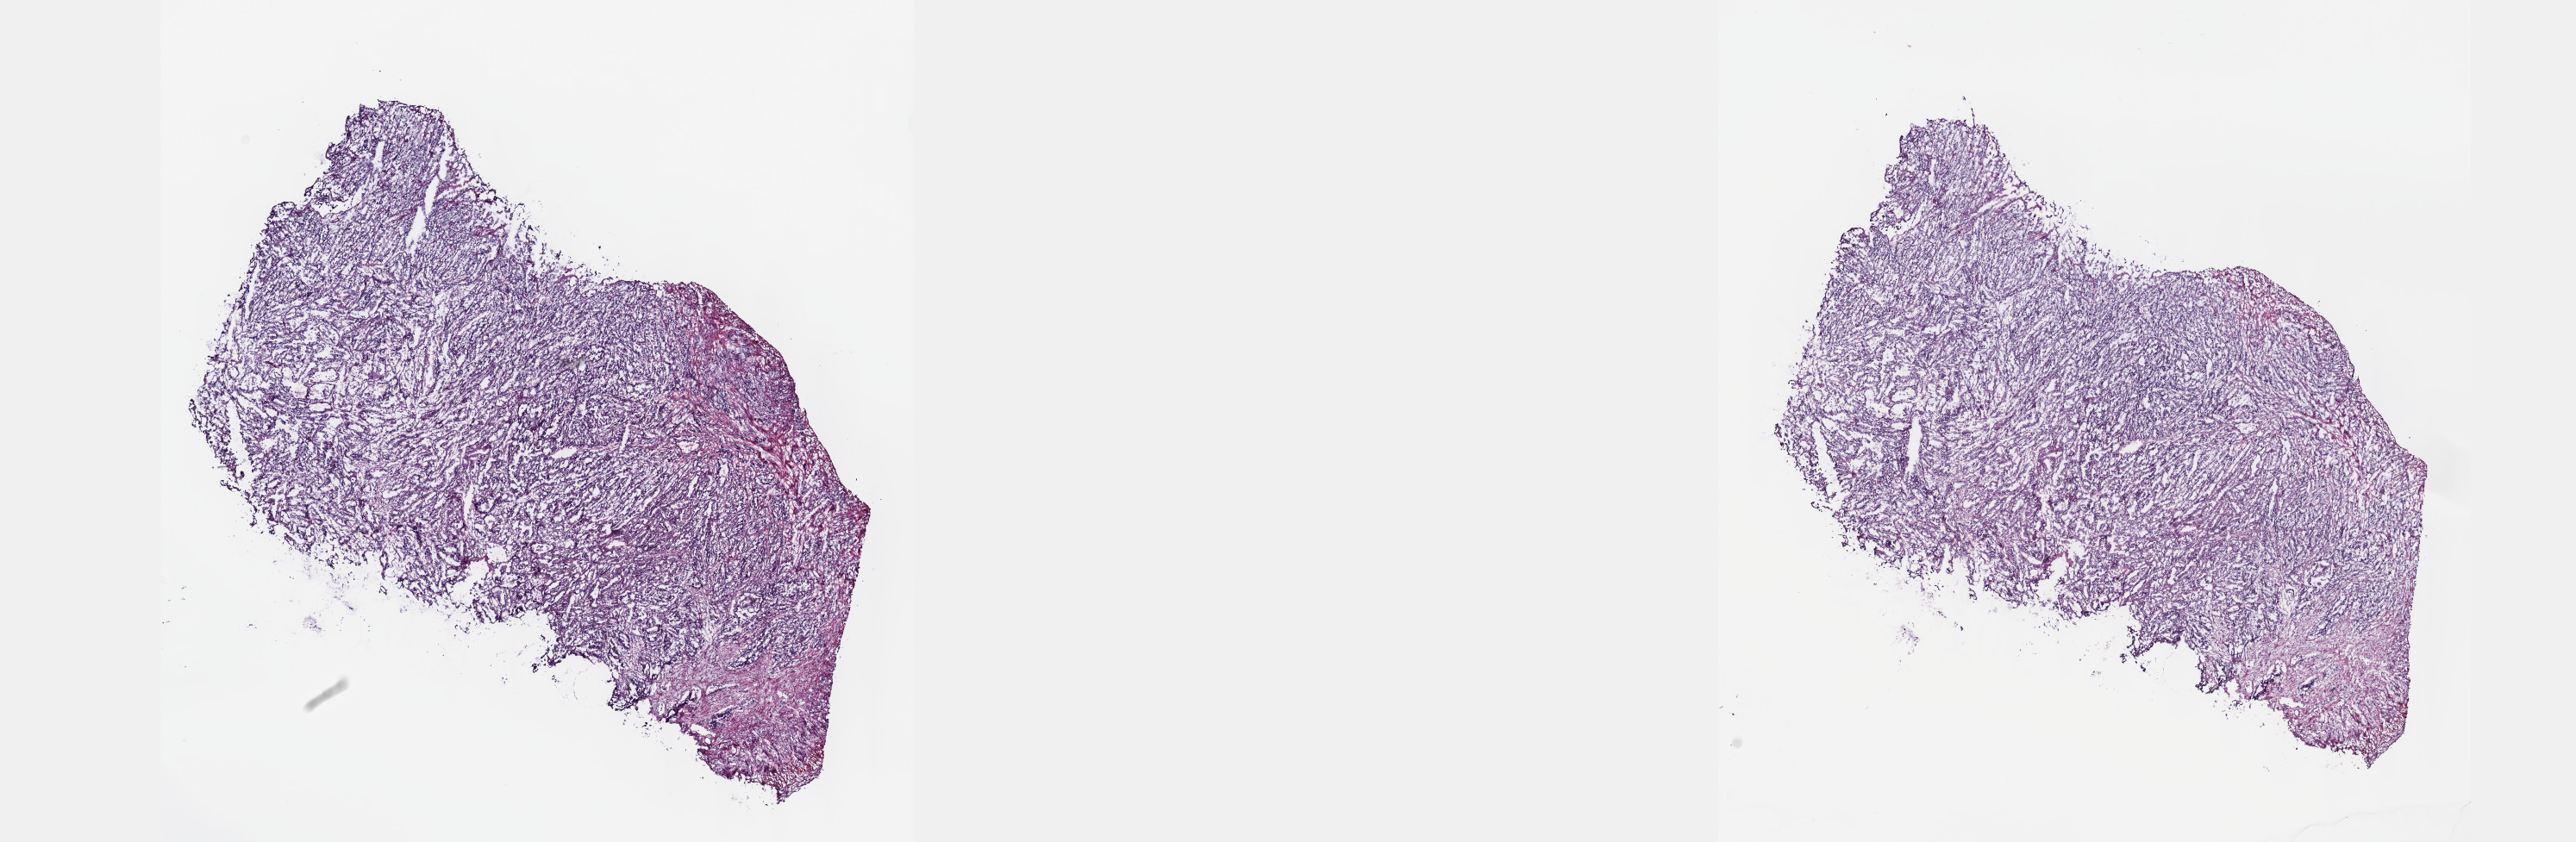
Whole-slide histology image, H&E — shown as a low-resolution overview of the whole scanned area (about 24.1 x 7.9 mm, from a 40x scan), frozen section, primary tumour sample from the esophagus. Male patient; age at initial diagnosis 58 years. Histologic grade: G3 (poorly differentiated). Pathologist review of this section (percent, as recorded): tumour cells 63%, tumour nuclei 80%, normal cells 0%, stromal cells 22%, necrosis 15%. Infiltration values recorded for this section: lymphocyte infiltration 10%, monocyte infiltration 2%, neutrophil infiltration 2%.
AJCC pathologic stage: IVA. Lymph nodes positive (case pathology): 9 of 13 examined. Diagnosis: Adenocarcinoma, NOS (lower third of esophagus).